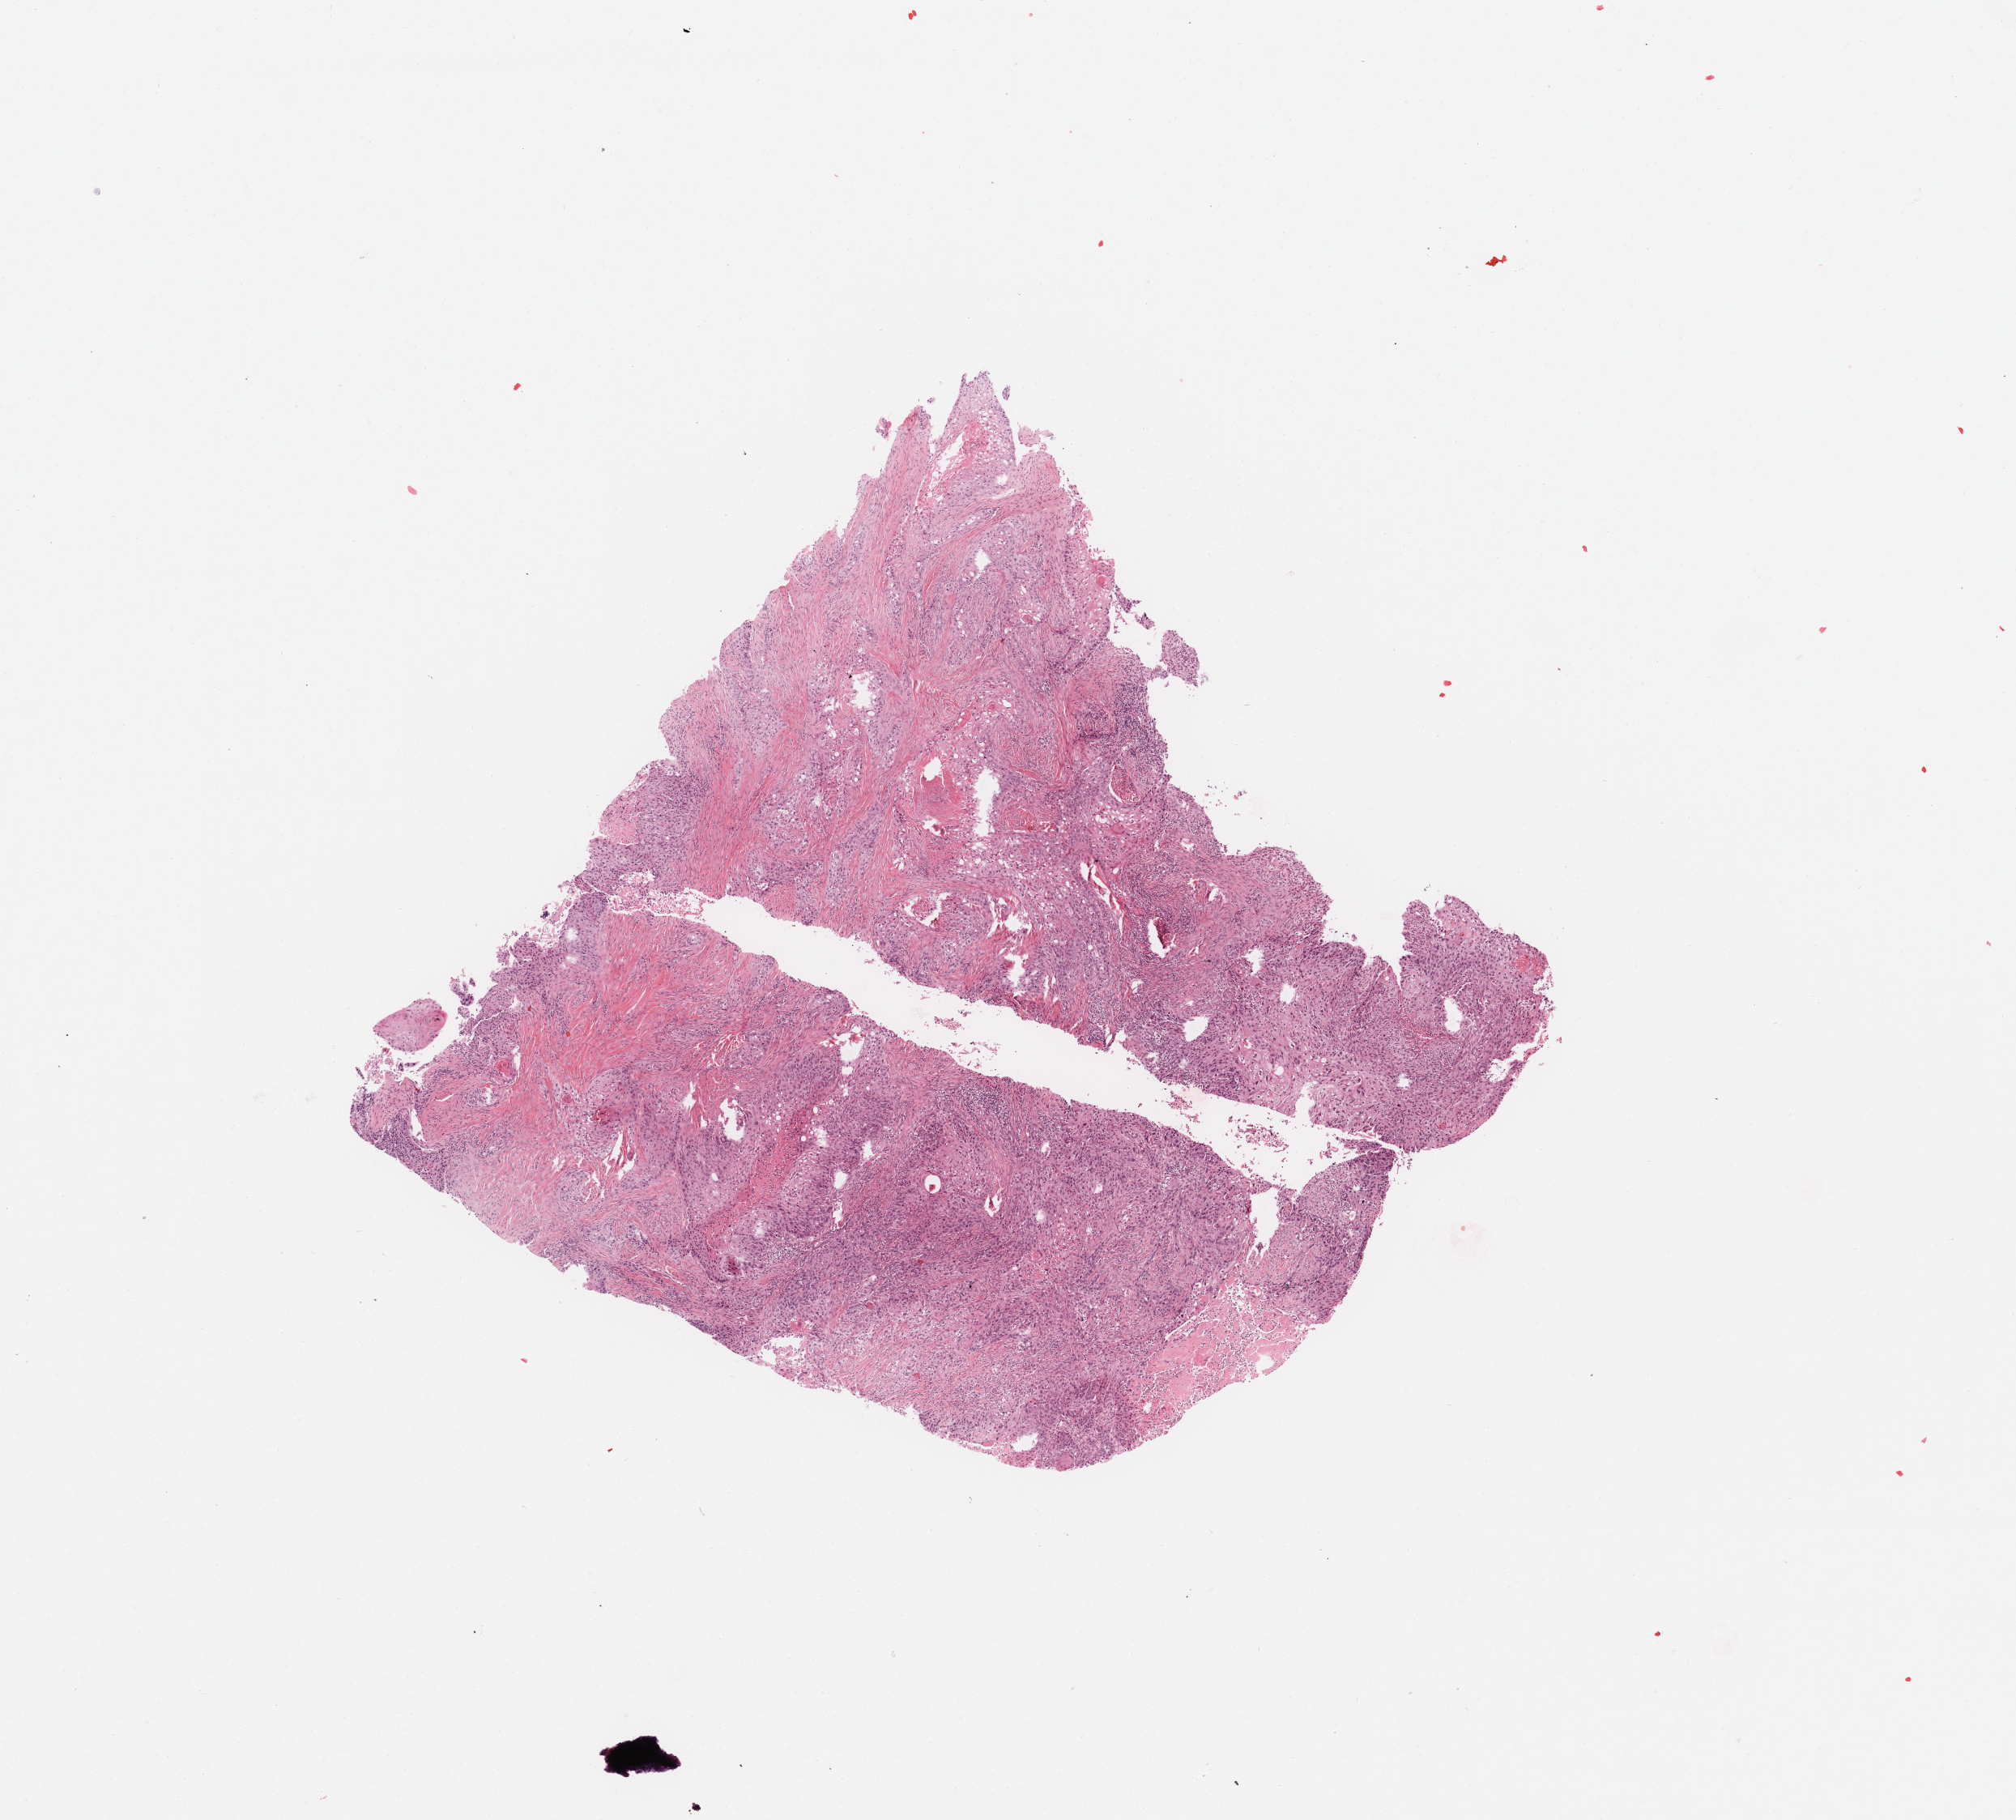
Whole-slide histology image, Hematoxylin and eosin (H&E) stained, a low-resolution overview of the entire scanned area, about 9.8 x 8.9 mm (slide scanned at 20x); tumour tissue sample, sampled site: larynx. 52-year-old male patient. Histologic grade: G1 (well differentiated). Slide review estimates, as recorded: tumour nuclei 80%, necrosis 5%.
* histologic diagnosis: Squamous cell carcinoma, NOS (larynx, NOS)
* AJCC pathologic stage: III
* primary tumour site (as recorded): larynx